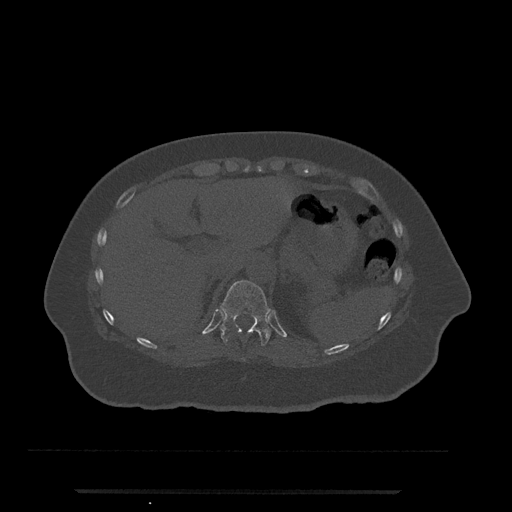
CT including the spine, one axial slice; position 242 of 797 along the scan axis; bone window (W 1800 / L 400 HU); 0.5 mm slice thickness; 512 × 512 image matrix. Patient: female, 51 years. From the clinical record (not read from this slice): primary cancer: neuro.
Structures marked on this image (semi-automatic segmentation, software-assisted and operator-edited):
- T11 vertebra: box from (x=220, y=280) to (x=273, y=346) px